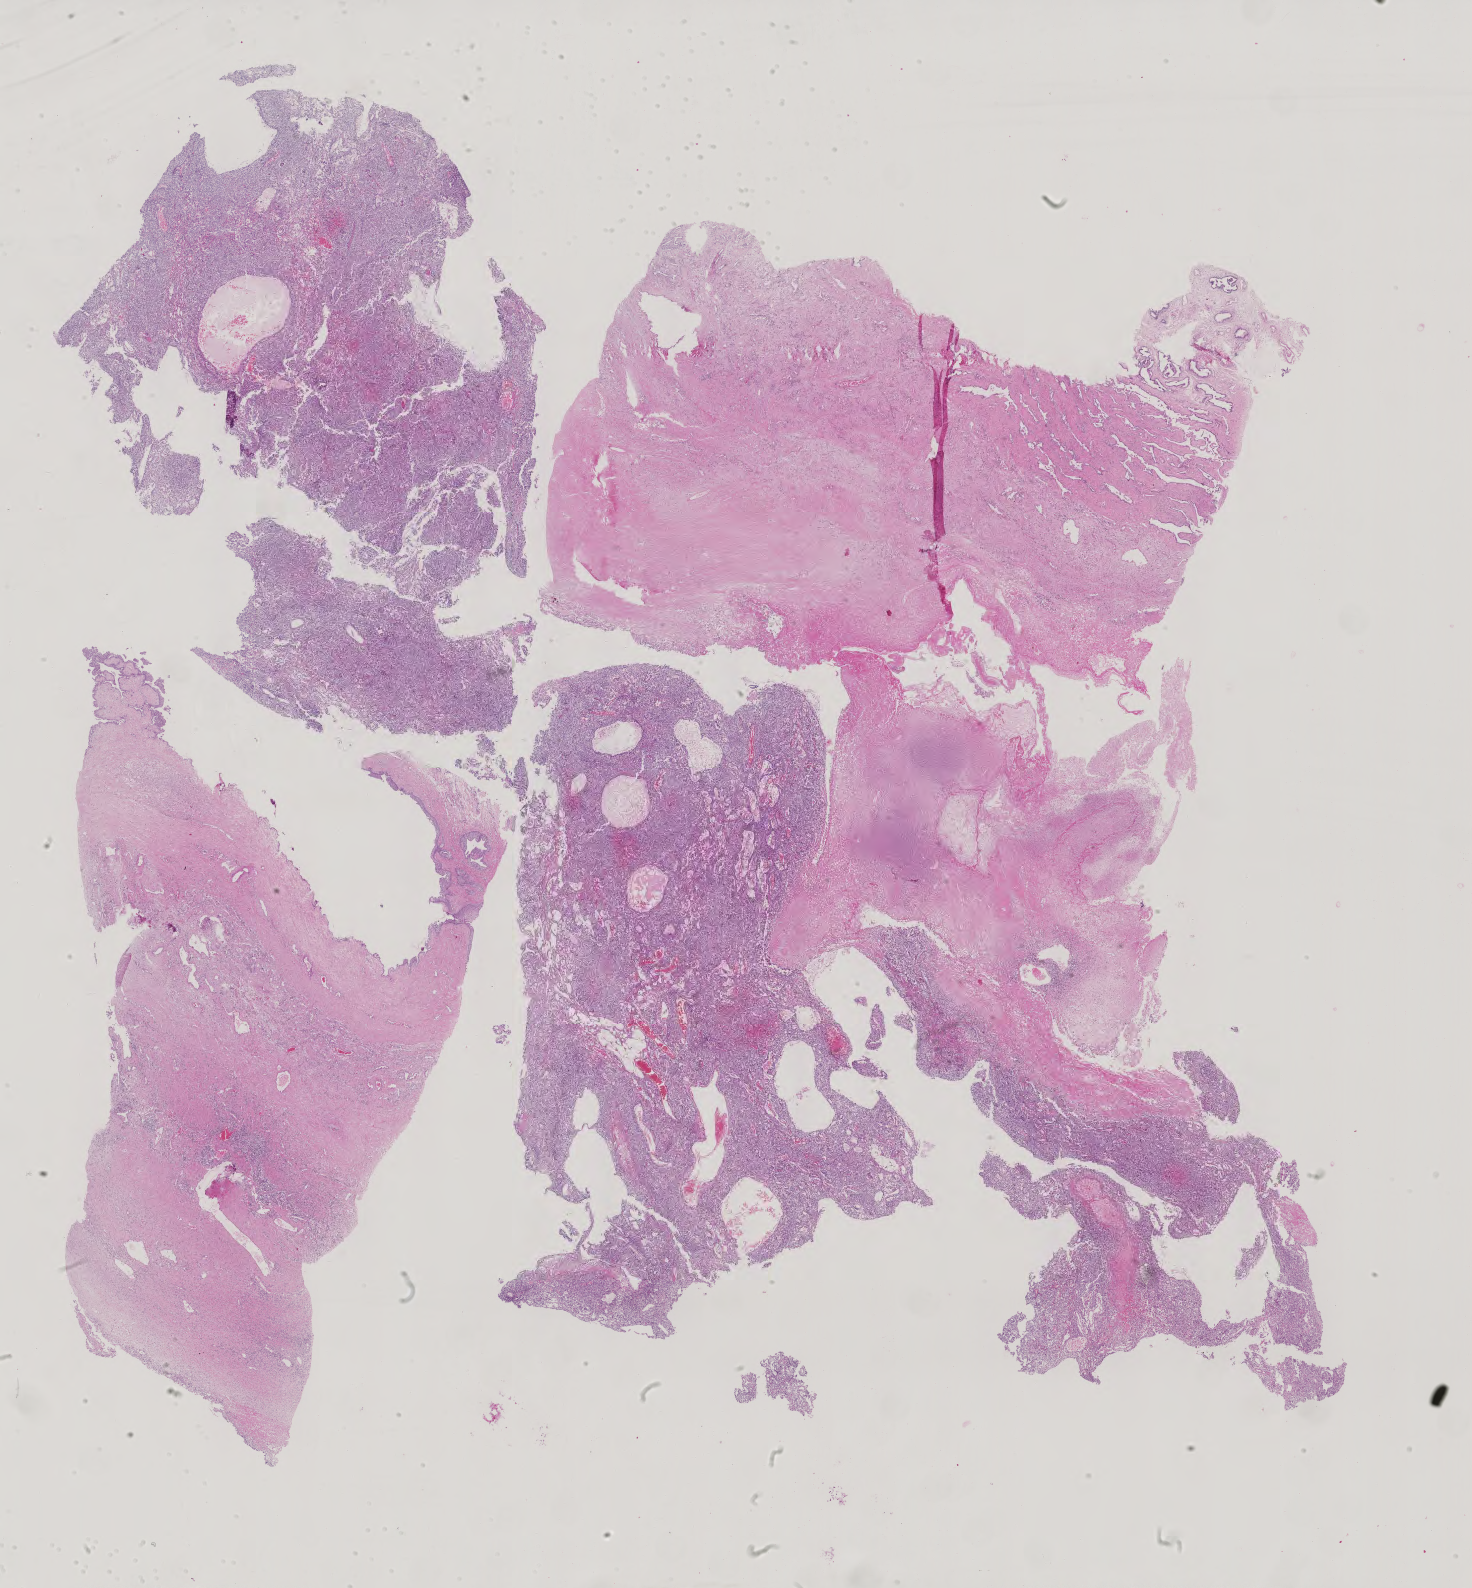
H&E whole-slide image — a low-resolution overview of the entire scanned area, about 21.5 x 23.1 mm. Male patient.
- specimen: formalin-fixed paraffin-embedded (FFPE) diagnostic section; sample: primary tumour, testis